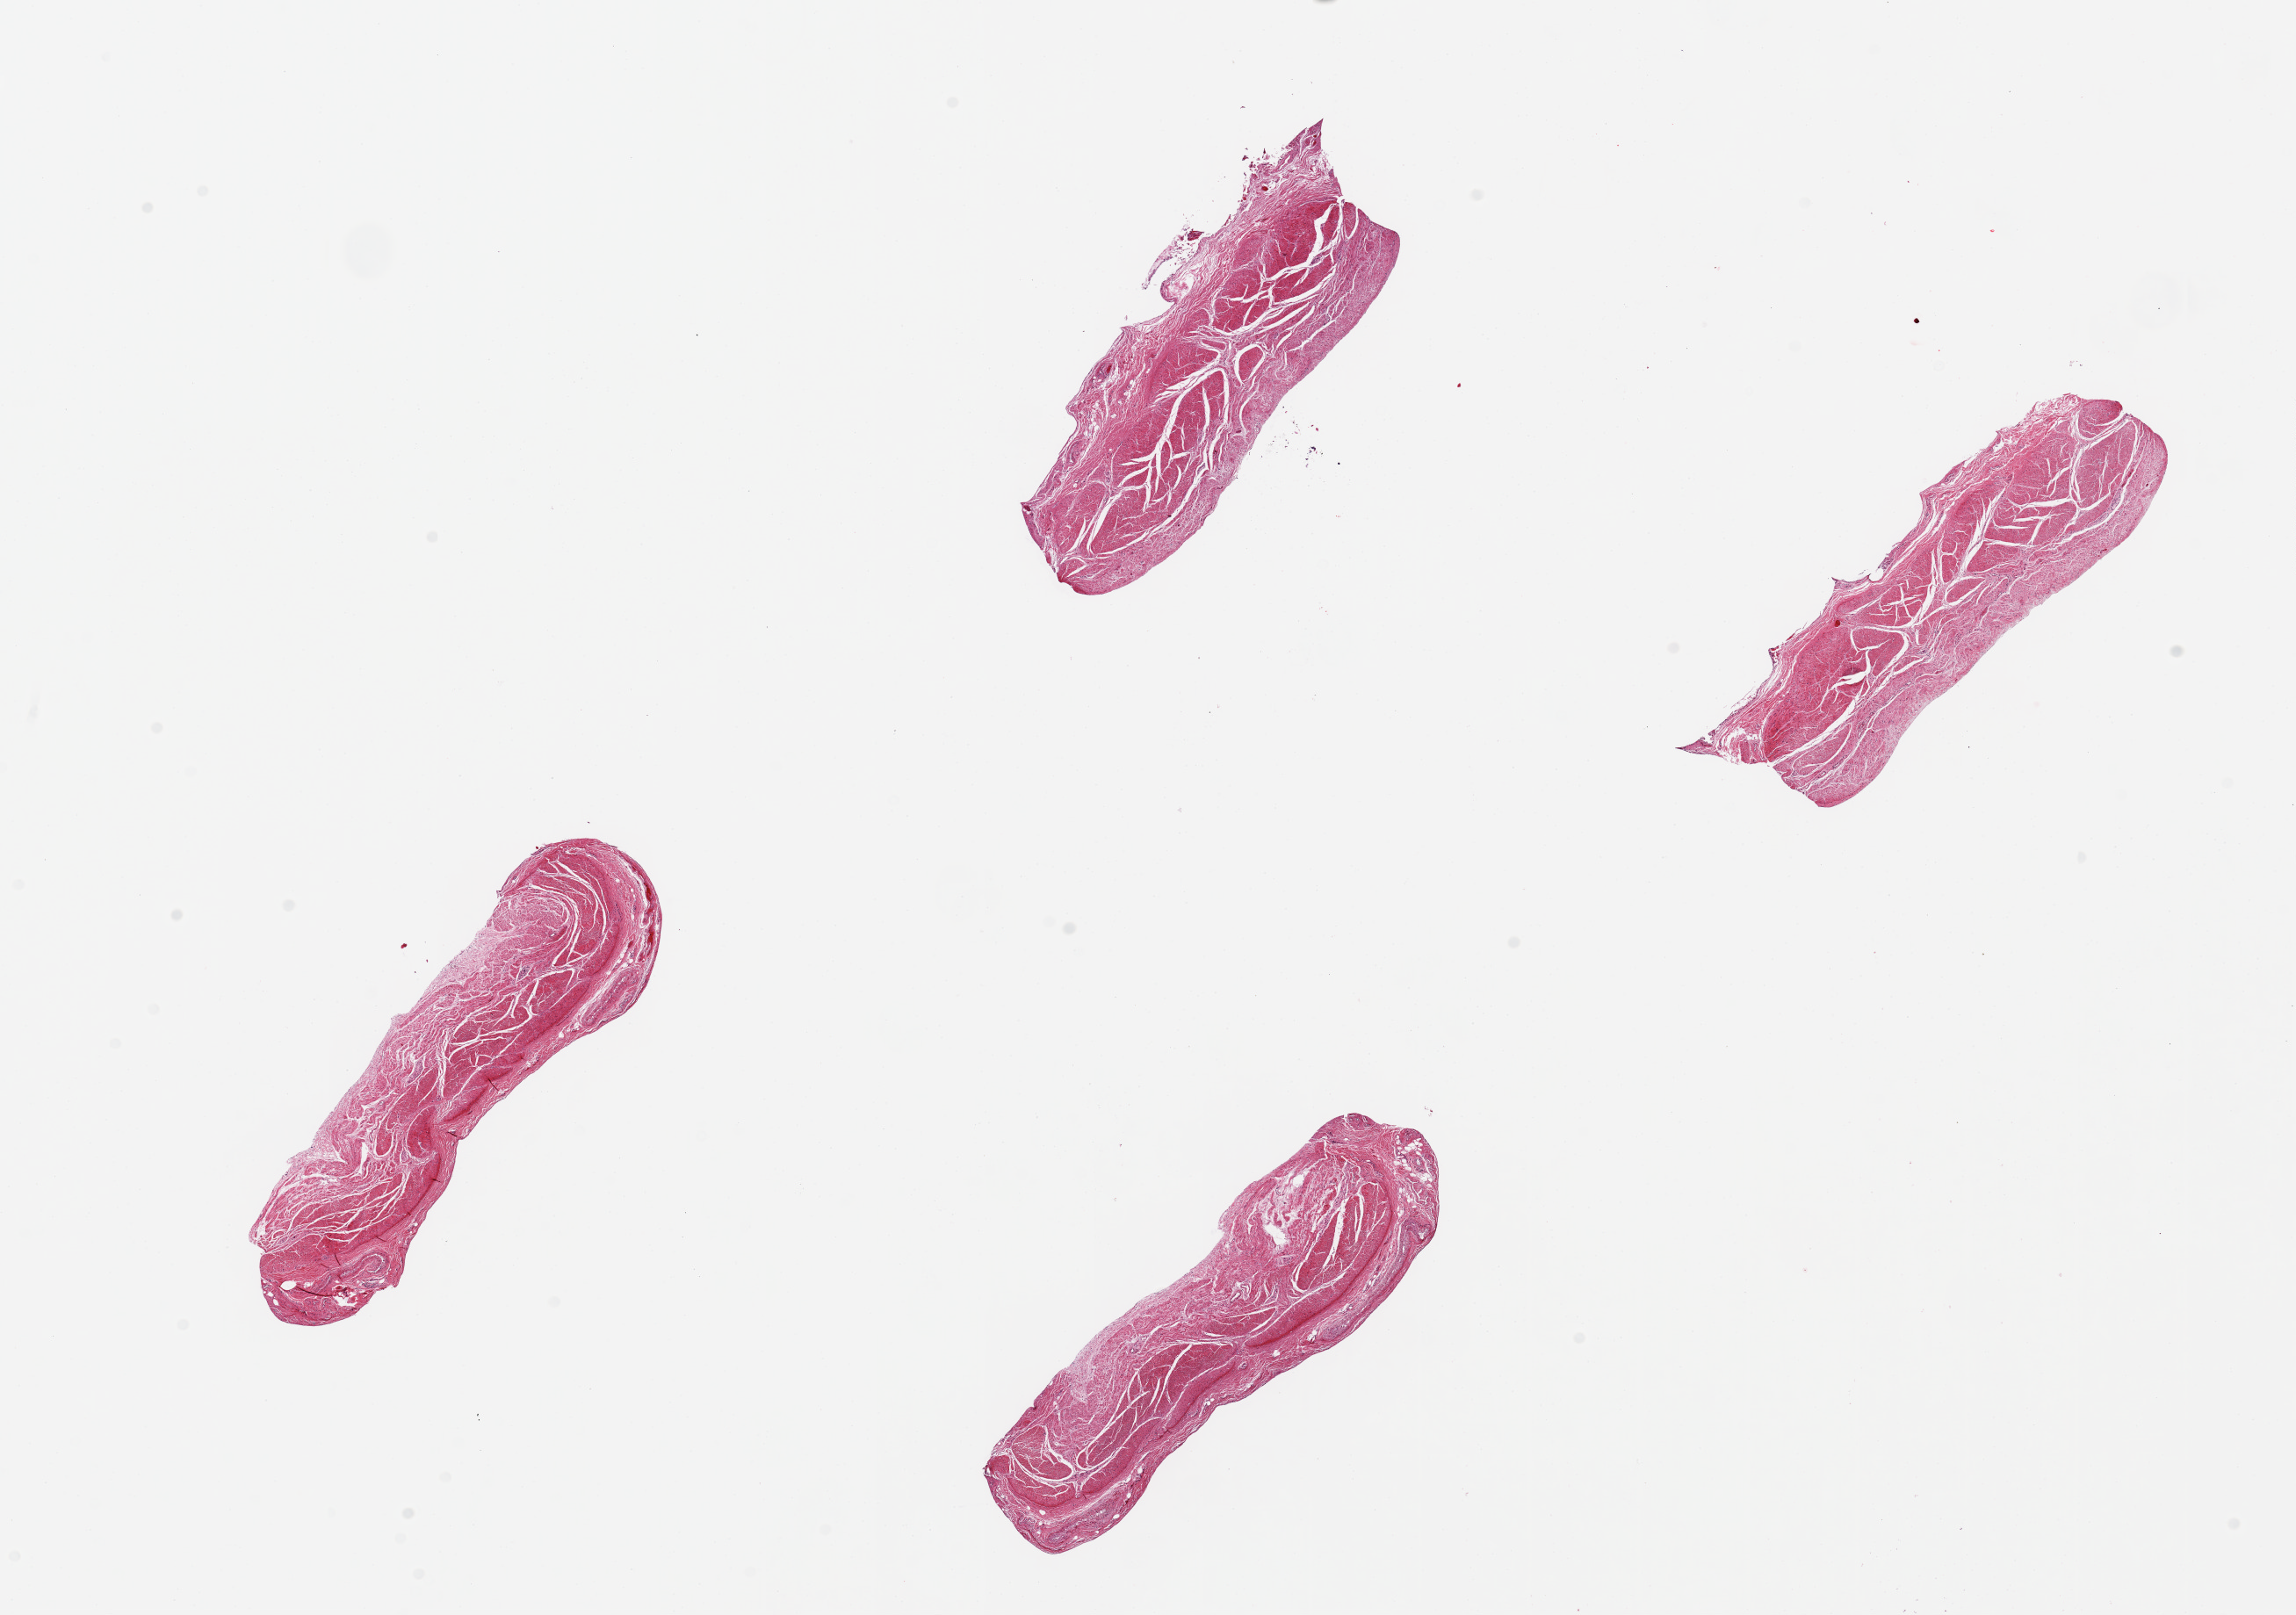
Hematoxylin and eosin (H&E) whole-slide image — shown as a low-resolution overview of the whole scanned area (about 20.7 x 14.5 mm, acquisition: 20x scan); PAXgene-fixed paraffin-embedded (PFPE) section; section of stomach (target tissue); donor tissue sample.
- reviewer comment on this tissue sample: 4 pieces, up to 5x1.5mm; muscle only